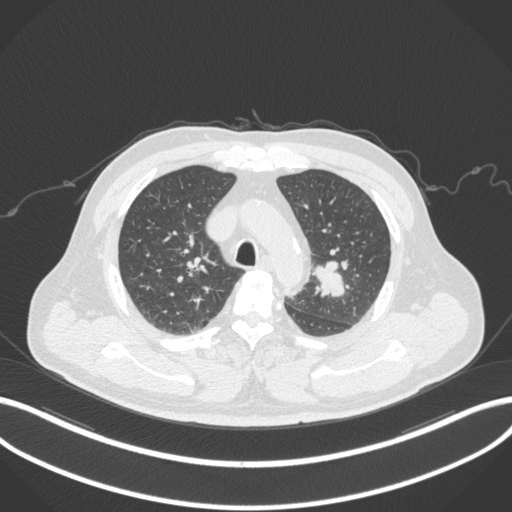
Chest CT, one axial slice. Position 226 of 286 along the scan axis. Reconstruction kernel B31f. Lung window (W 1500 / L -600 HU). 512 × 512 image matrix, field of view 400 × 400 mm. Patient: male, 67 years. Case-level facts recorded for this patient, not image findings: clinical TNM (as recorded): T2a N1 M0.
Outlined on this slice (rectangle marked by the reading radiologist):
- lung tumour (recorded histology: adenocarcinoma): bounding box <310,254,352,302> (left, top, right, bottom; pixels)